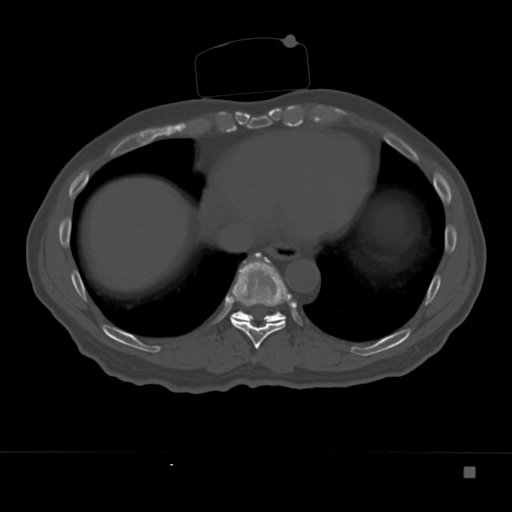
CT including the spine, one axial slice. Slice 184 of 332 in the series (ordered by position). Reconstruction kernel Br40s. 120 kVp. Bone window (W 1800 / L 400 HU). 1.5 mm slice thickness. 512 × 512 image matrix, field of view 389 × 389 mm. Patient: male, 72 years. Case-level facts recorded for this patient, not image findings: primary cancer: skeletal.
Annotated regions visible in this slice (semi-automatic segmentation, software-assisted and operator-edited):
- T10 vertebra: bounding box (x1, y1, x2, y2) in pixels: (230, 262, 284, 321)
- T9 vertebra: (230, 253, 291, 349)